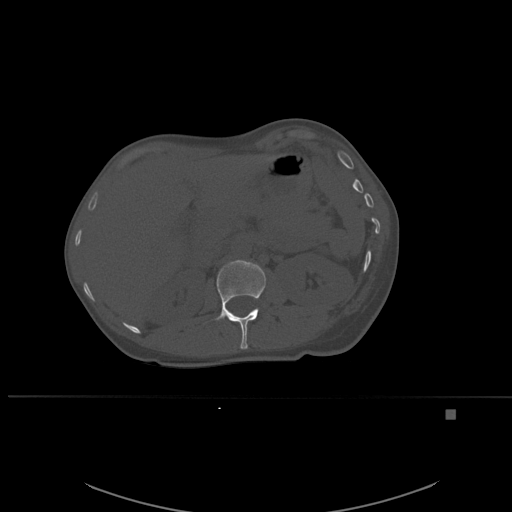
CT including the spine, one axial slice; slice 257 of 537 in the series (ordered by position); bone window (W 1800 / L 400 HU); 1.5 mm slice thickness; 512 × 512 image matrix, field of view 440 × 440 mm. Female patient, age 45 years. From the clinical record (not read from this slice): primary cancer: lung.
Annotated regions visible in this slice (semi-automatic segmentation, software-assisted and operator-edited):
- L1 vertebra: bounding box (x1, y1, x2, y2) in pixels: (215, 260, 266, 349)